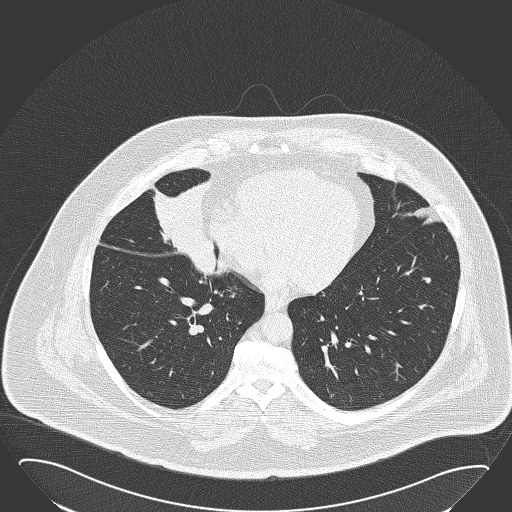
Low-dose screening chest CT, axial slice; first (baseline) screen; lung window (W 1500 / L -600 HU); 2 mm slice thickness; lung (sharp) reconstruction kernel (B50f); 512 × 512 image matrix, field of view 432 × 432 mm. Male participant, aged 61 years at enrolment. Former smoker at enrolment.
Expert reader's lesion annotation, bounding box <133,171,227,261> (left, top, right, bottom; pixels). The screening reader recorded 2 non-calcified nodules or masses ≥4 mm on this exam (right middle lobe, left lower lobe); which of them this box marks is not recorded. Participant outcome: lung cancer diagnosed 47 days after this screen — basaloid squamous cell carcinoma, right middle lobe, right hilum, poorly differentiated (G3), stage IIB (AJCC 6th edition), 95 mm at pathology.